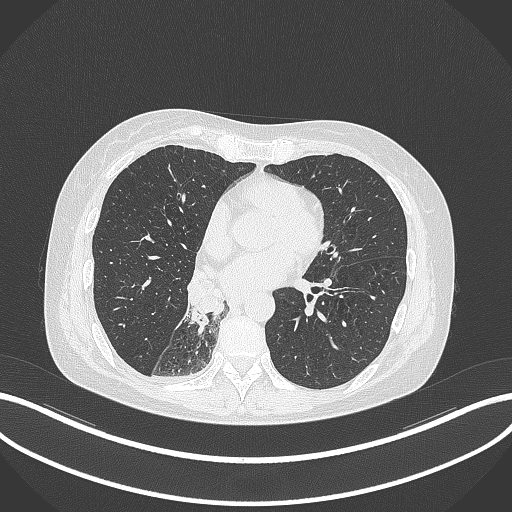
Chest CT, one axial slice. Position 134 of 329 along the scan axis. Reconstruction kernel B70f. Lung window (W 1500 / L -600 HU). 1 mm slice thickness. 512 × 512 image matrix. Patient: female, 63 years. Case-level facts recorded for this patient, not image findings: clinical TNM (as recorded): T1c N0 M0.
Structures marked on this image (rectangle marked by the reading radiologist):
- lung tumour (recorded histology: adenocarcinoma): bounding box <182,267,230,333> (left, top, right, bottom; pixels)